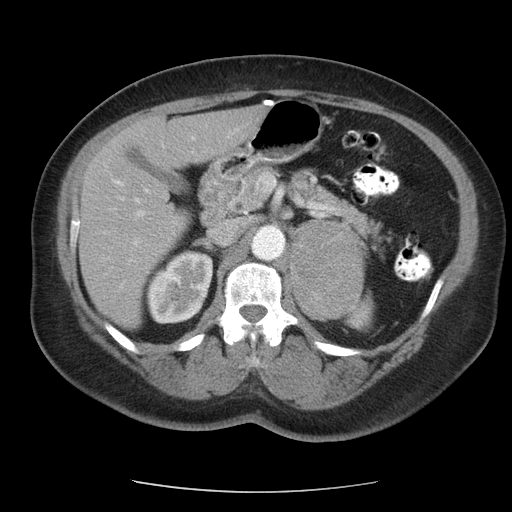
Contrast-enhanced abdominal CT, one axial slice. Position 65 of 95 along the scan axis. Reconstruction kernel STANDARD. 120 kVp. Soft-tissue window (W 400 / L 40 HU). 512 × 512 image matrix. Patient: female, 71 years. Case-level facts recorded for this patient, not image findings: diagnosis: adrenocortical carcinoma; tumour side: left adrenal; tumour size at pathology: 8.8 cm.
Outlined on this slice (semi-automatic segmentation, software-assisted and operator-edited):
- mass: box from (x=291, y=221) to (x=364, y=318) px